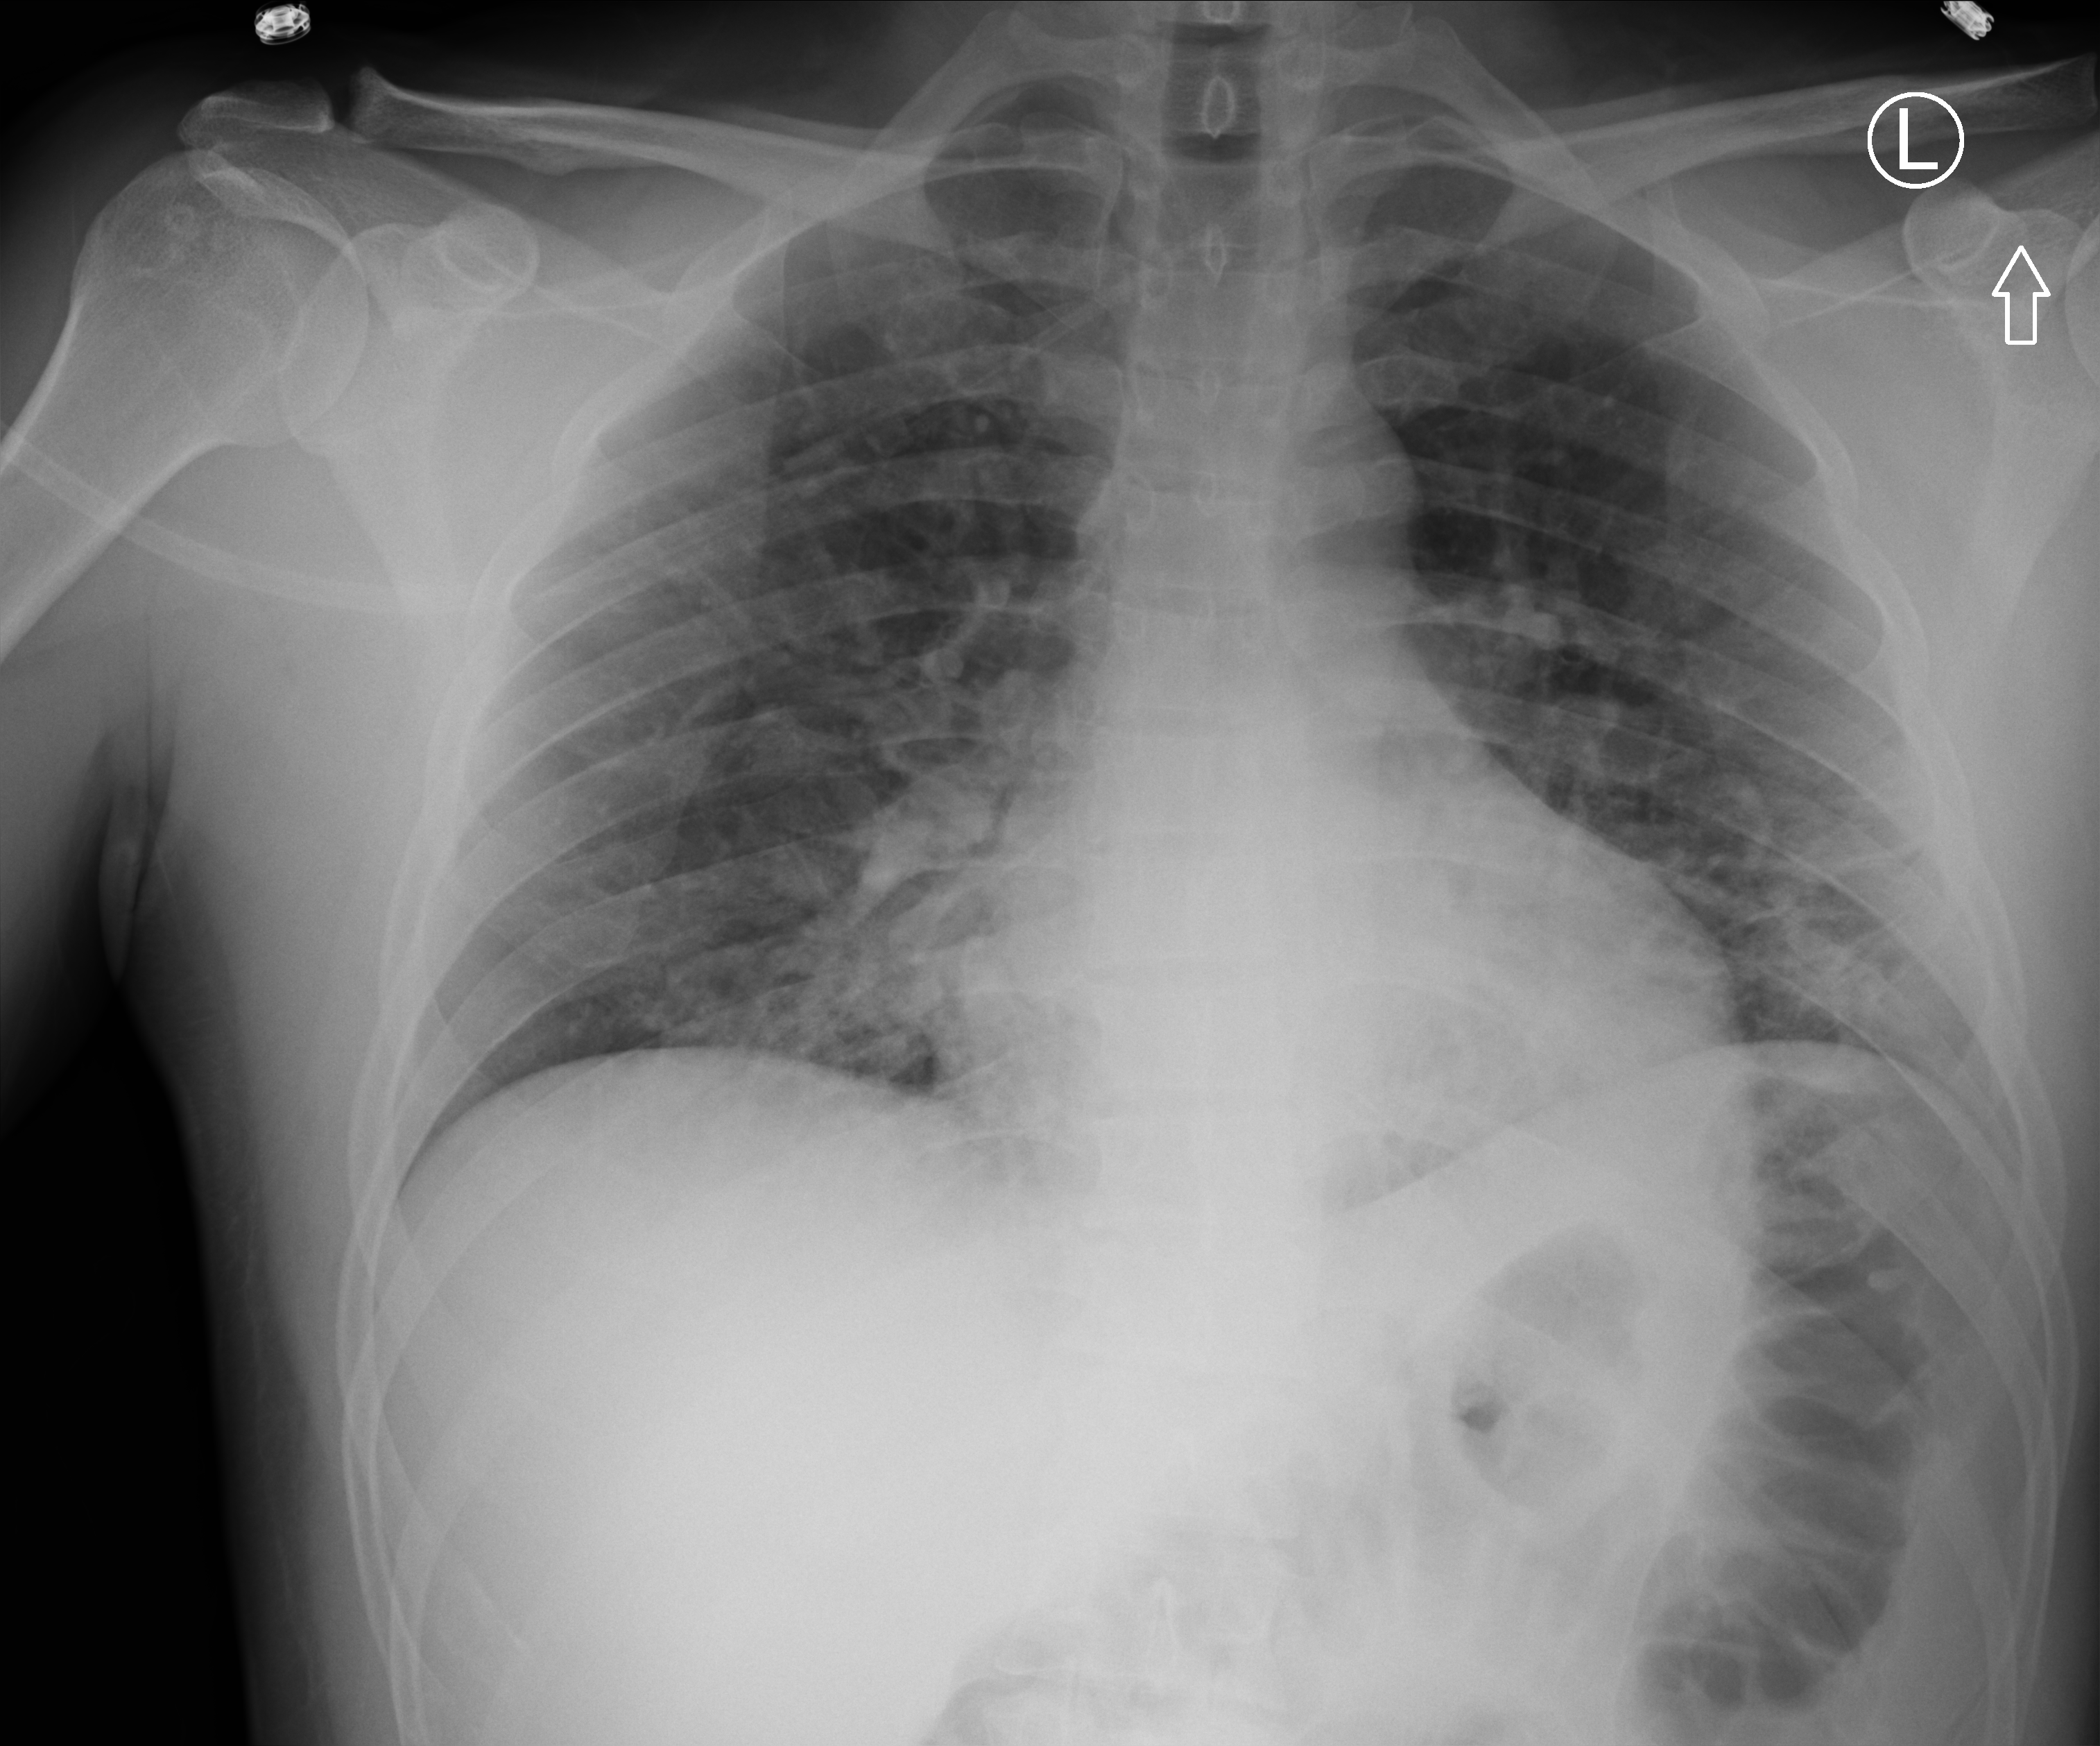
Portable chest radiograph; anteroposterior (AP) projection. Patient hospitalised with COVID-19; male, aged 18–59 years.
Admission-level facts for this patient (not findings on this image; timing relative to this image not recorded):
- admitted to intensive care during this hospital stay: no